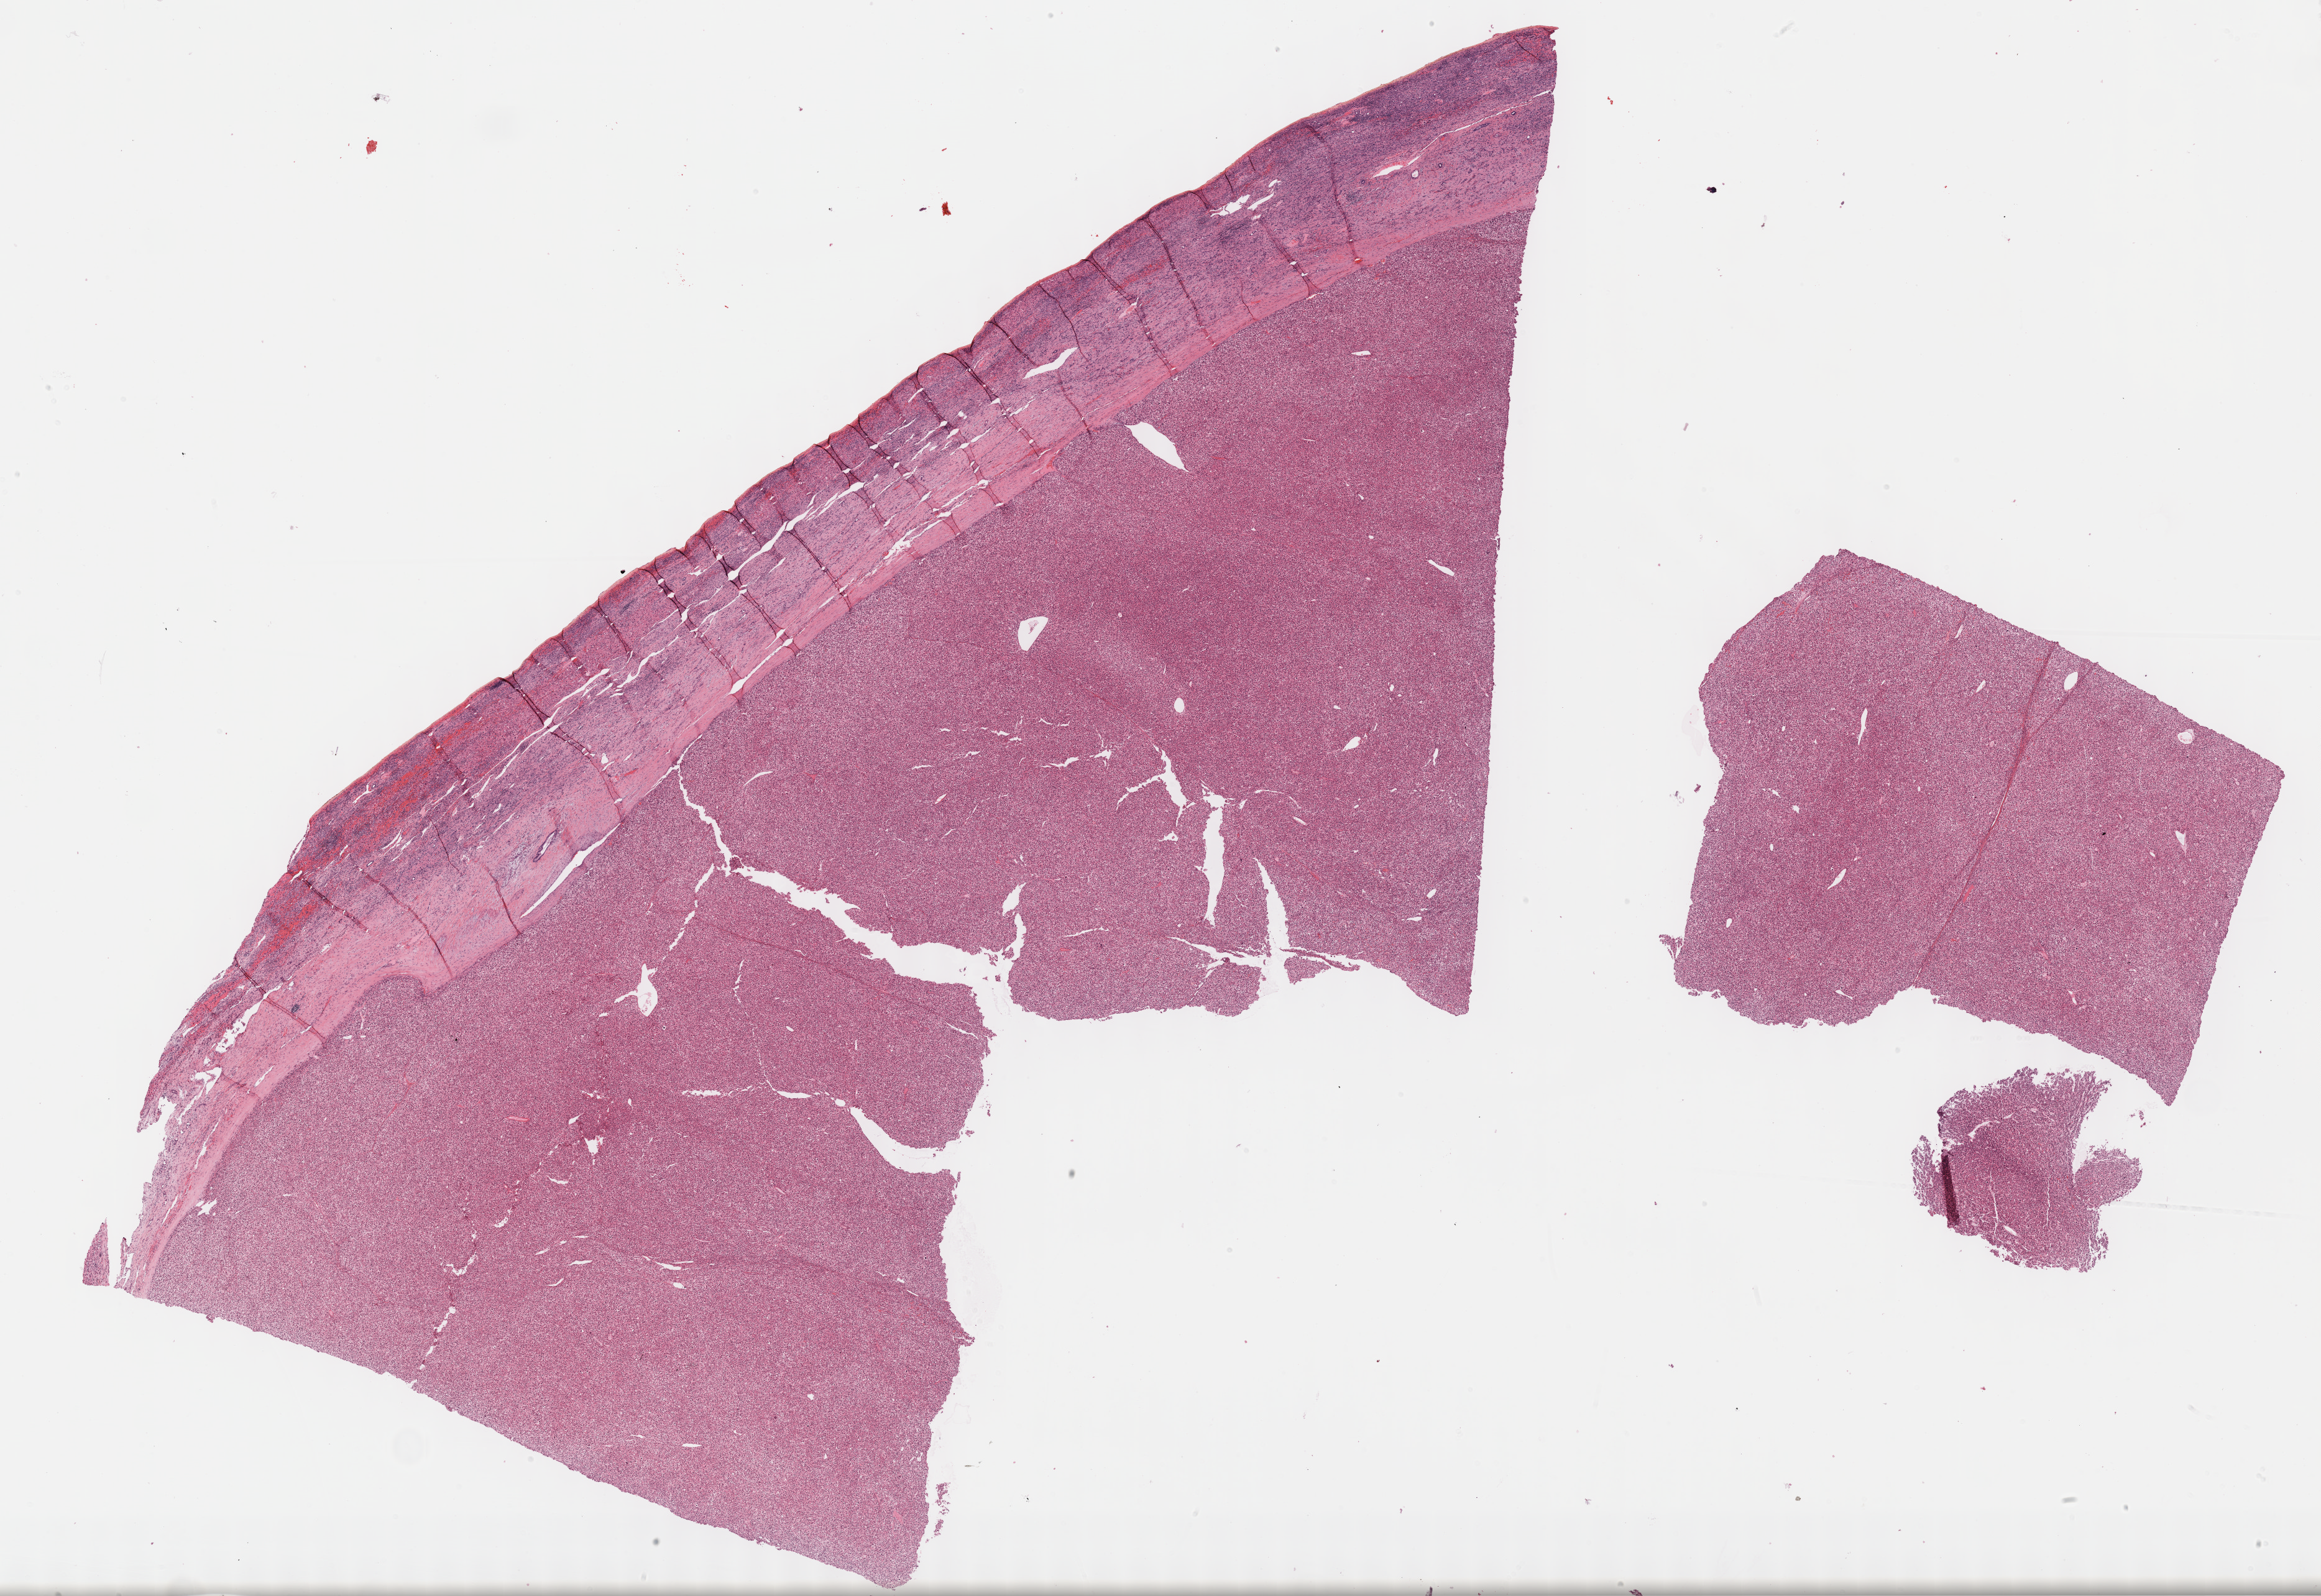
Digitized H&E tissue section (whole slide) — whole scanned area (about 30.2 x 20.8 mm, slide scanned at 40x) shown as a low-resolution overview, formalin-fixed paraffin-embedded (FFPE) diagnostic section, liver, primary tumour sample. Female patient; age at initial diagnosis 63 years.
Pathologic diagnosis: Hepatocellular carcinoma, NOS.